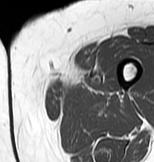
MRI of an extremity soft-tissue mass, one axial slice. Slice 3 of 83 in the series (ordered by position). MR volume resampled by the dataset authors to the PET/CT grid (not the native acquisition matrix). 154 × 162 image matrix, field of view 150 × 158 mm. Female patient. Case-level facts recorded for this patient, not image findings: histological type: myxofibrosarcoma; grade: intermediate; site of the primary tumour: left thigh.
Outlined on this slice (expert contour drawn on MRI and transferred to this co-registered scan by the dataset authors):
- gross tumour volume including surrounding oedema: bounding box (x1, y1, x2, y2) in pixels: (51, 70, 109, 97)